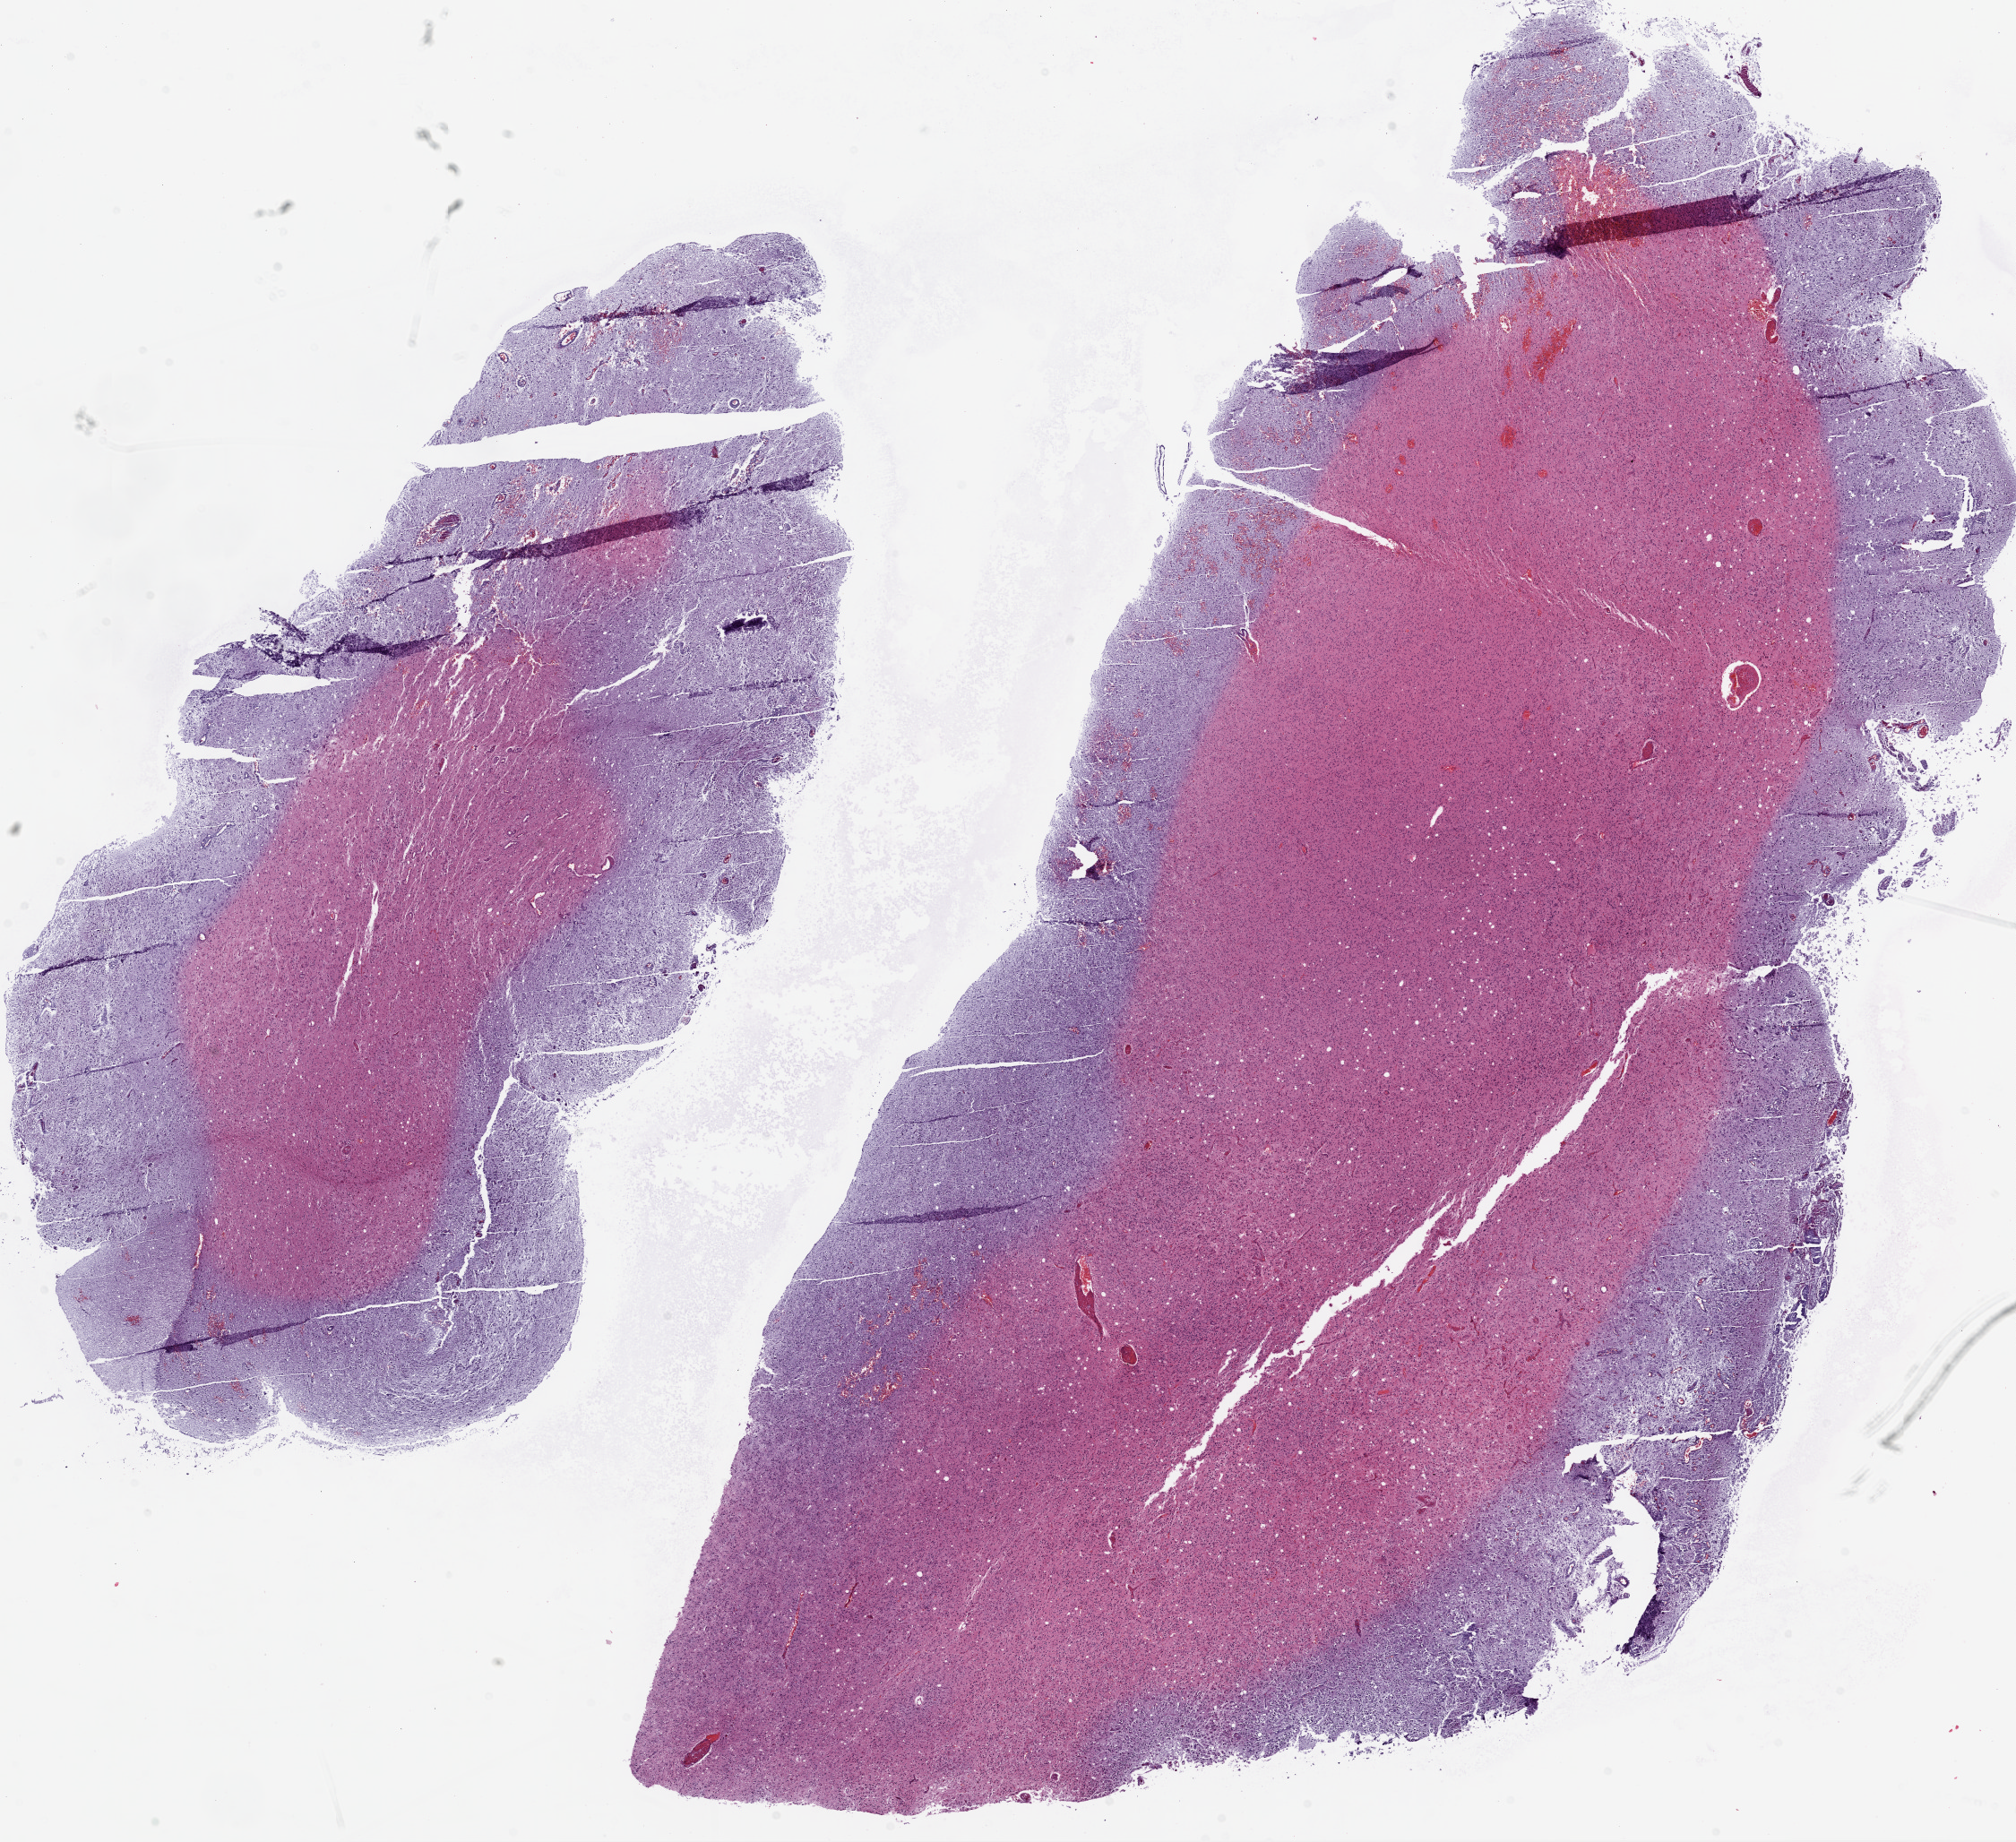
Digitized H&E tissue section (whole slide), a low-resolution overview of the entire scanned area, about 18.1 x 16.5 mm; formalin-fixed paraffin-embedded (FFPE) diagnostic section; primary tumour sample from the brain. Patient: female, age at initial diagnosis 70 years.
Pathologic diagnosis: Glioblastoma.